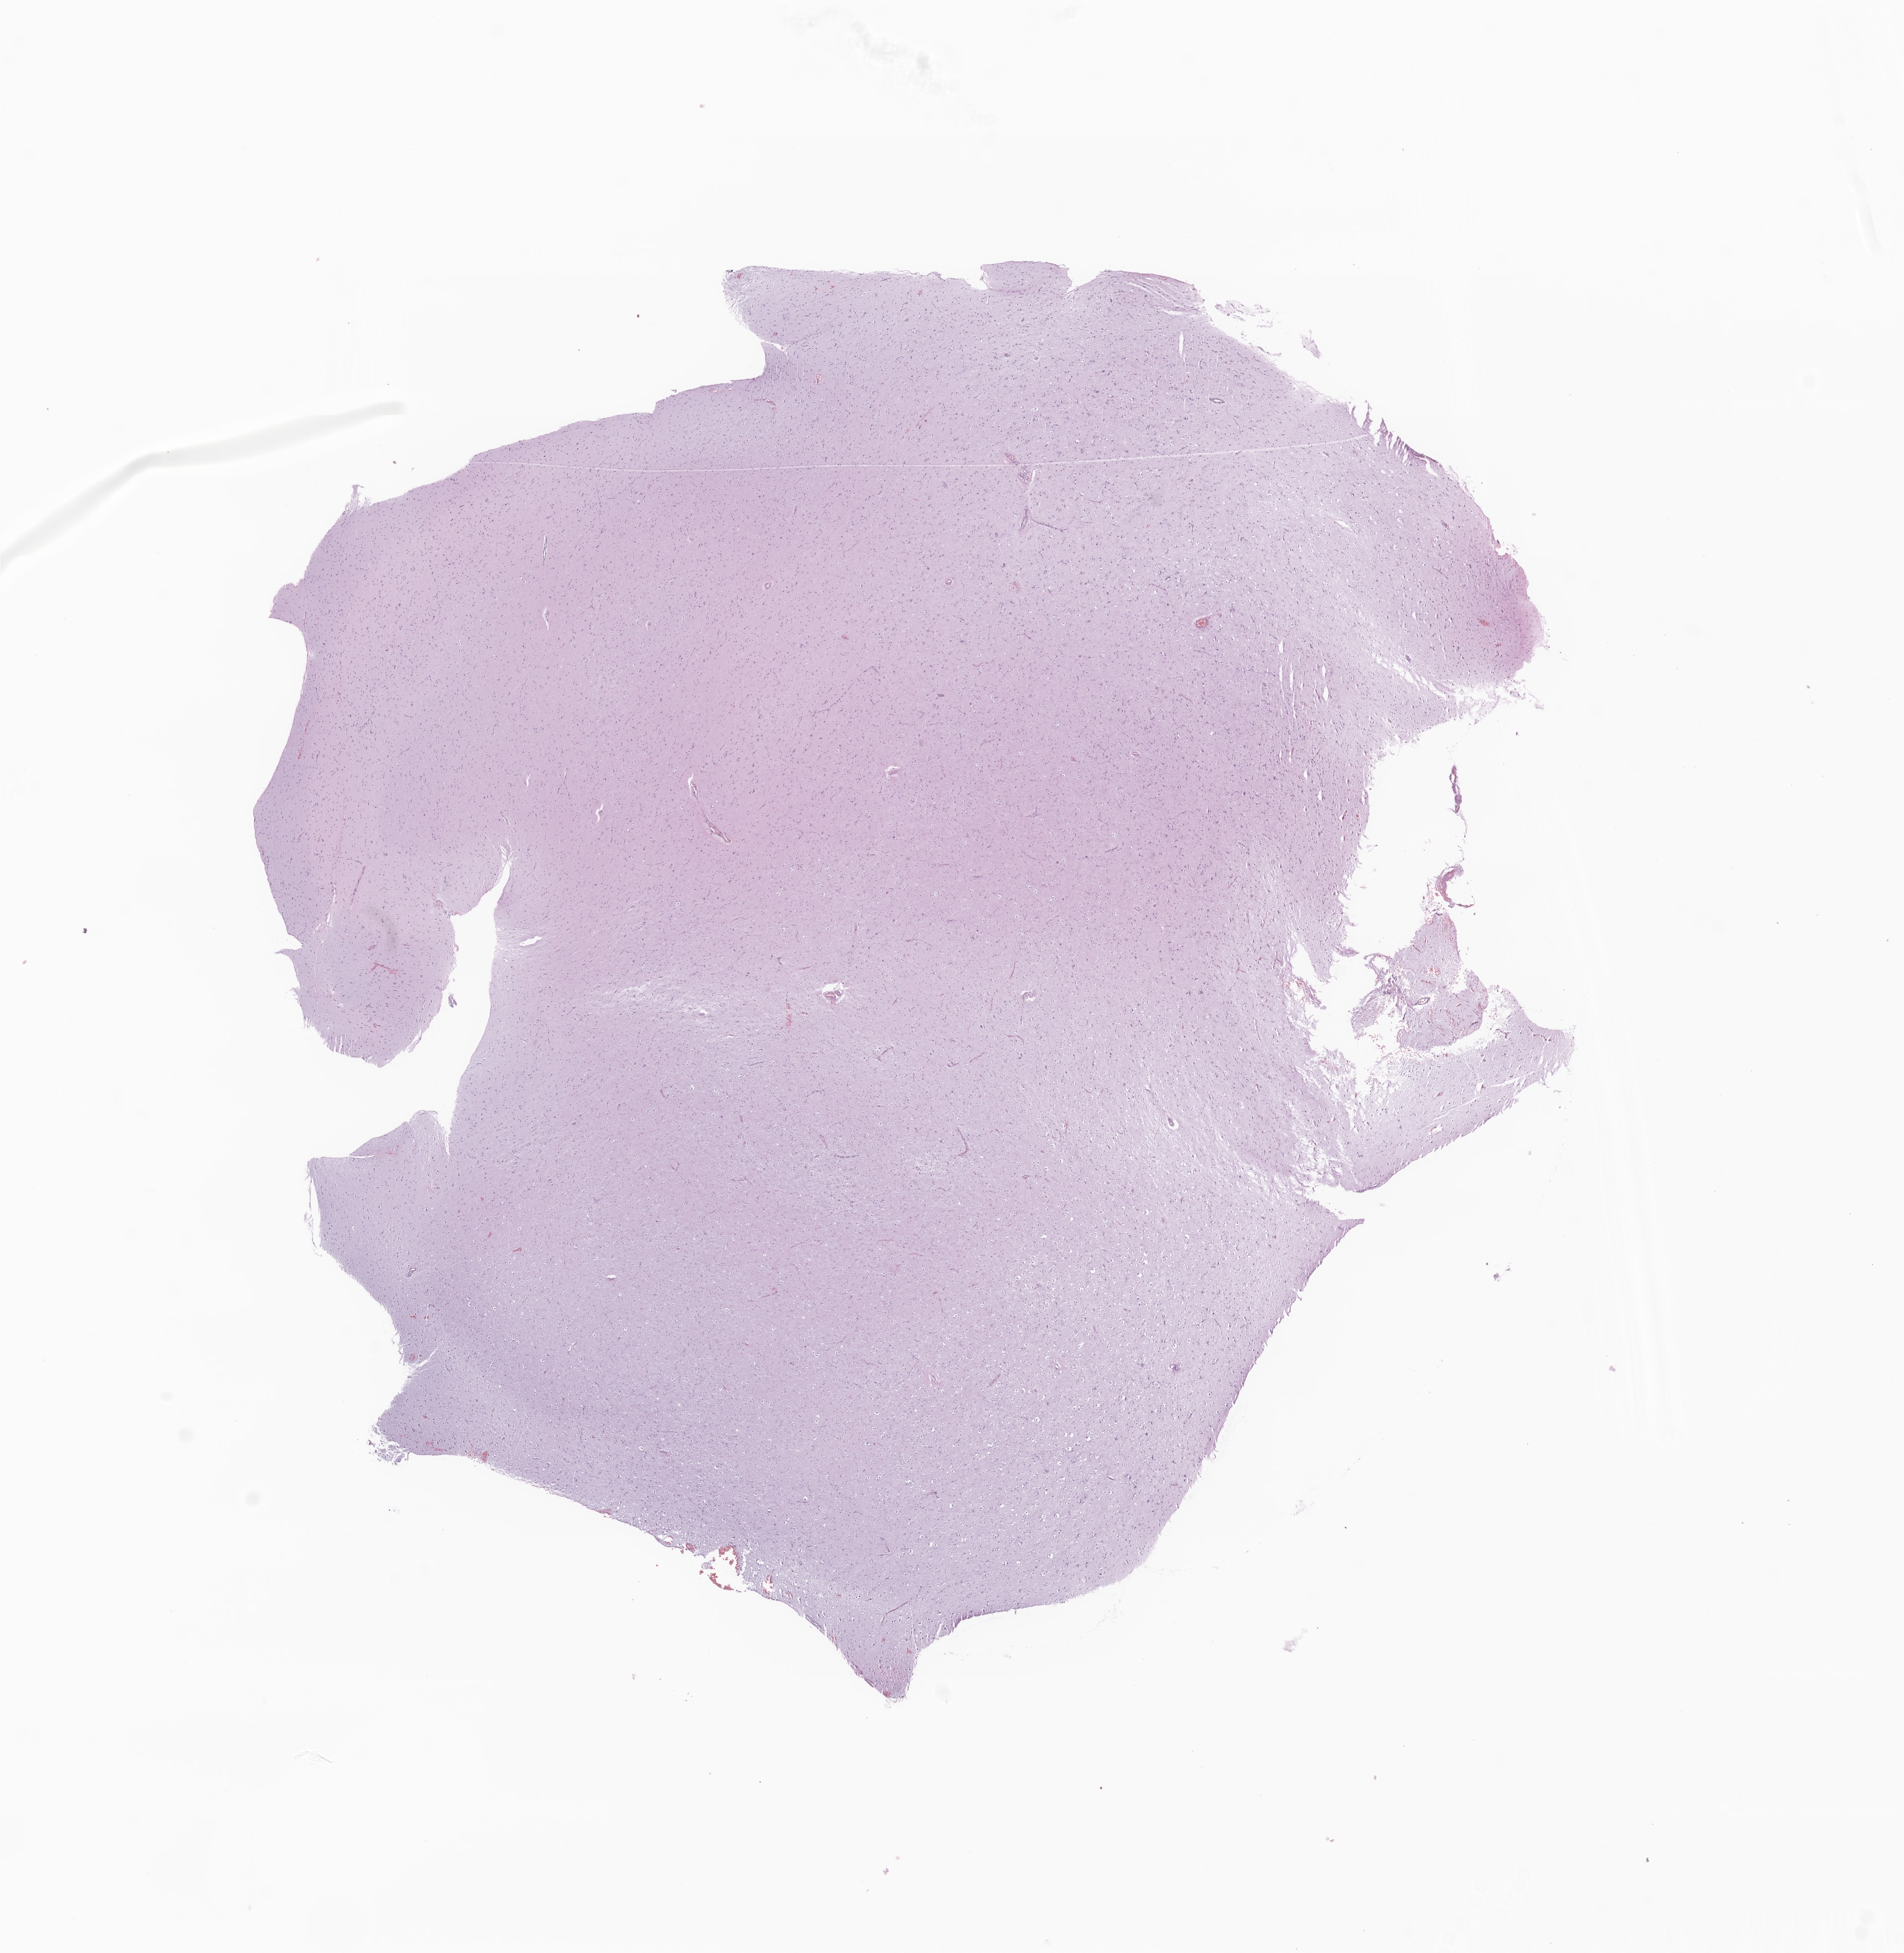
Whole-slide image, H&E stain of tumor tissue from the brain — whole scanned area (about 14.5 x 14.9 mm) shown as a low-resolution overview. Formalin-fixed paraffin-embedded section. Male patient, age 204 months (17 years).
* recorded diagnosis: Glioma, malignant